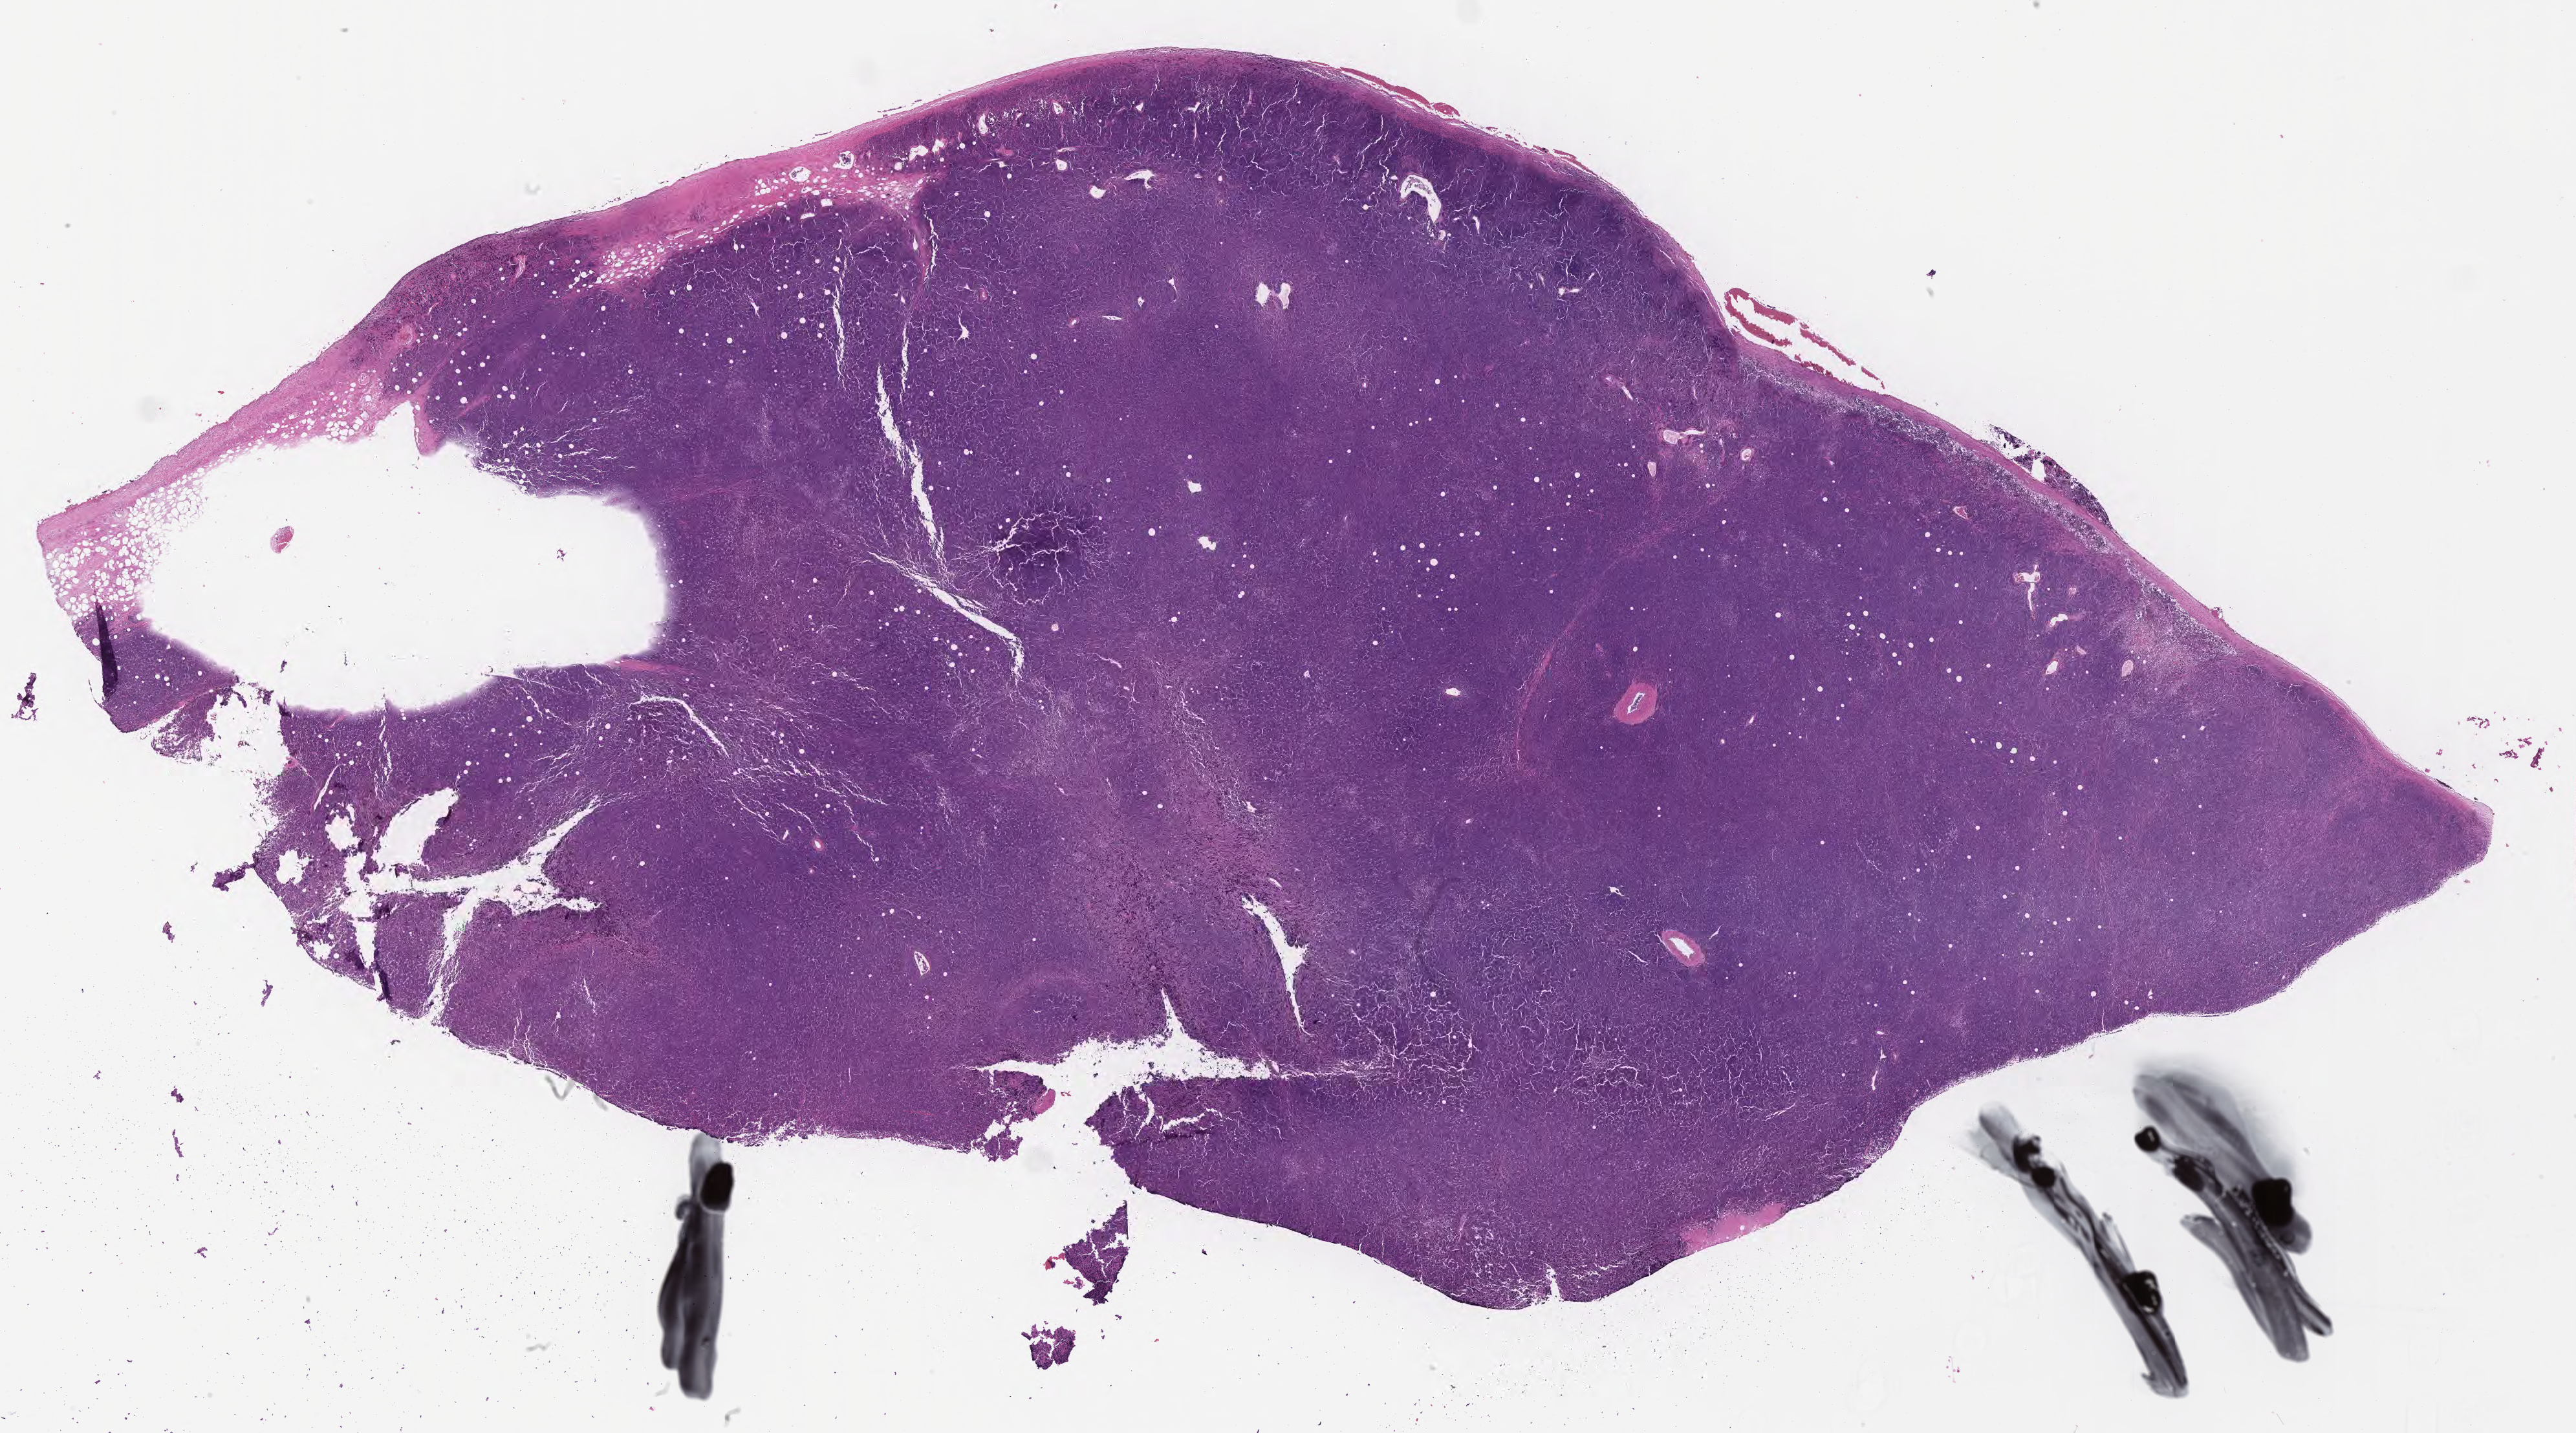
Haematoxylin and eosin whole-slide image, shown as a low-resolution overview of the whole scanned area (about 32.2 x 17.9 mm), tumor tissue. Patient male; 51 years old.
Histologic diagnosis: Burkitt lymphoma, NOS.